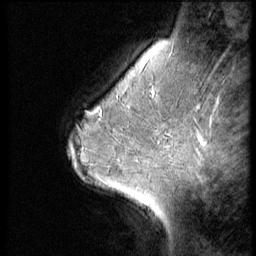
Breast MRI (dynamic contrast-enhanced), one sagittal slice; position 43 of 56 along the scan axis; 3 images stored at this slice position (order not interpretable as contrast timing); 1.5 T; TE 4.2 ms, TR 9 ms; 256 × 256 image matrix, field of view 180 × 180 mm. Patient: female, 45 years. Case-level facts recorded for this patient, not image findings: setting: breast cancer imaged before/during neoadjuvant chemotherapy; receptor status: HR-positive, HER2-negative.
Annotated regions visible in this slice (semi-automatically segmented with operator editing):
- analysis volume of interest (the breast-tissue region the enhancement analysis was run in; not a lesion): bounding box (x1, y1, x2, y2) in pixels: (102, 77, 166, 129)
- tumour enhancement mask (voxels above the 140 % enhancement threshold inside the analysis volume of interest): (151, 90, 154, 95)